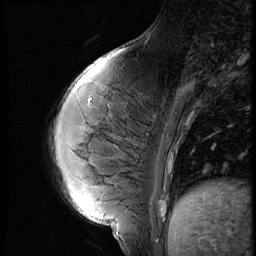
Breast MRI (dynamic contrast-enhanced), one sagittal slice; position 18 of 56 along the scan axis; 3 images stored at this slice position (order not interpretable as contrast timing); 1.5 T; TE 4.2 ms, TR 9 ms; 2.5 mm slice thickness; 256 × 256 image matrix, field of view 180 × 180 mm. Patient: female, 35 years. From the clinical record (not read from this slice): setting: breast cancer imaged before/during neoadjuvant chemotherapy; receptor status: HR-positive, HER2-negative.
Structures marked on this image (semi-automatically segmented with operator editing):
- analysis volume of interest (the breast-tissue region the enhancement analysis was run in; not a lesion): bounding box (x1, y1, x2, y2) in pixels: (58, 70, 171, 208)
- tumour enhancement mask (voxels above the 140 % enhancement threshold inside the analysis volume of interest): (163, 162, 171, 208)